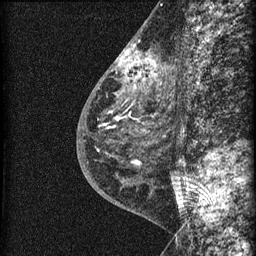
Breast MRI (dynamic contrast-enhanced), one sagittal slice; slice 26 of 60 in the series (ordered by position); dynamic contrast-enhanced series, image 2 of 3 at this slice position (ordered by acquisition); 1.5 T; TE 4.2 ms, TR 22.7 ms; 256 × 256 image matrix, field of view 180 × 180 mm. Female patient, age 48 years. Case-level facts recorded for this patient, not image findings: setting: breast cancer imaged before/during neoadjuvant chemotherapy; receptor status: triple-negative.
Annotated regions visible in this slice (semi-automatically segmented with operator editing):
- analysis volume of interest (the breast-tissue region the enhancement analysis was run in; not a lesion): bounding box [x1, y1, x2, y2] px = [115, 34, 169, 162]
- tumour enhancement mask (voxels above the 90 % enhancement threshold inside the analysis volume of interest): [119, 45, 157, 83]